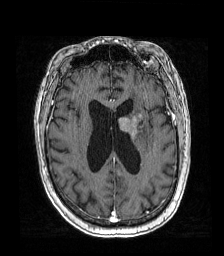
Brain MRI from a brain-tumour surgery series, one axial slice; position 68 of 192 along the scan axis; T1-weighted post-contrast; 1 mm slice thickness; 224 × 256 image matrix, field of view 219 × 250 mm. From the clinical record (not read from this slice): histopathology: Metastatic carcinoma from lung primary.
Outlined on this slice (outlined manually by an expert reader):
- tumour: box from (x=120, y=114) to (x=144, y=137) px